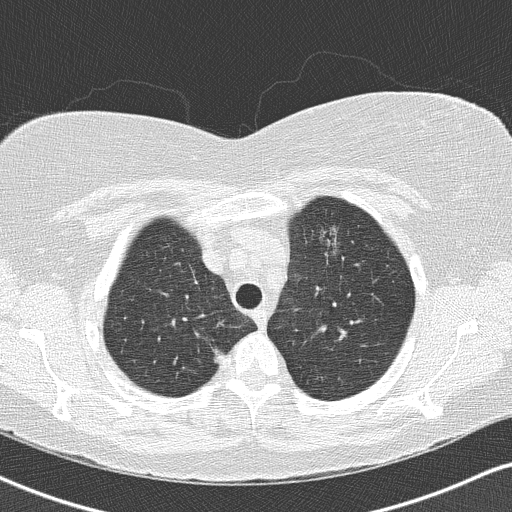
Low-dose screening chest CT, one axial slice. Position 117 of 146 along the scan axis. Reconstruction kernel B50f. 120 kVp. Lung window (W 1500 / L -600 HU). 2 mm slice thickness. 512 × 512 image matrix, field of view 328 × 328 mm.
Structures marked on this image (manually delineated by an expert):
- lesion 1 (tumor, upper lobe of left lung): box from (x=319, y=226) to (x=340, y=256) px